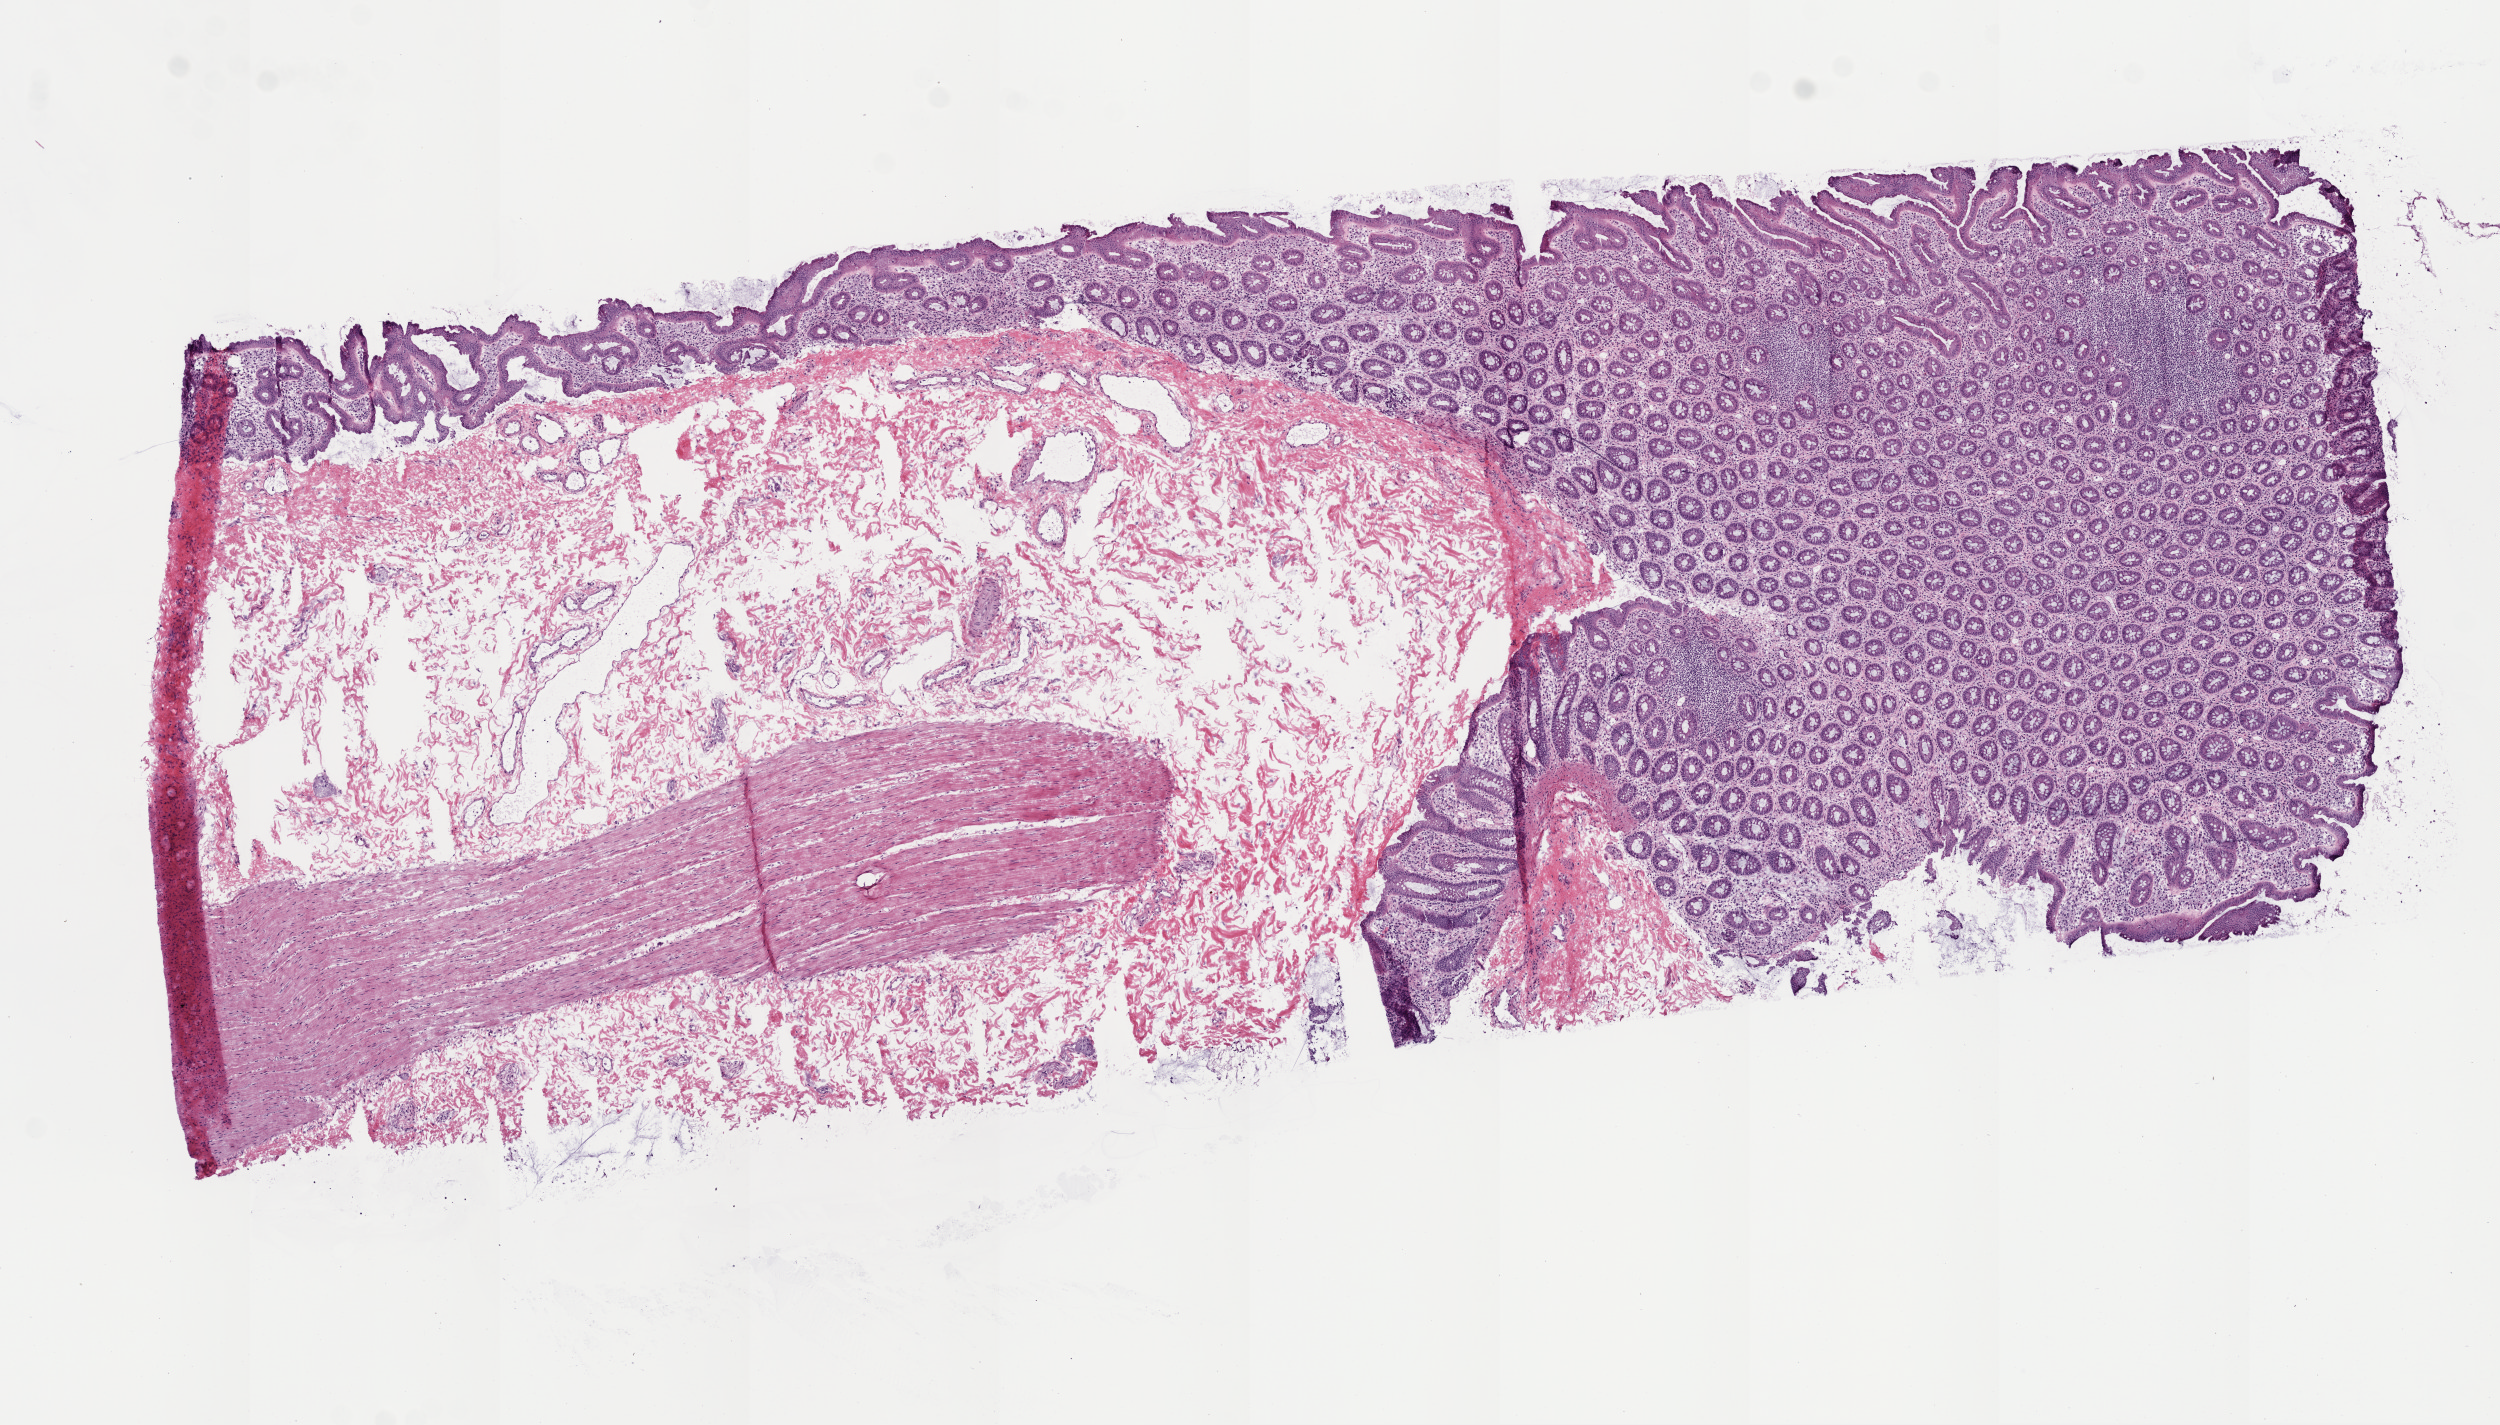
Whole-slide histology image, H&E-stained, shown as a low-resolution overview of the whole scanned area (about 10.0 x 5.7 mm). Frozen section from the top of the tissue portion. Rectum, solid tissue normal (non-tumour tissue) sample. Female patient; age at initial diagnosis 48 years.
* this section: solid tissue normal sample (biorepository sample class)
* patient diagnosis: Adenocarcinoma, NOS (rectosigmoid junction)